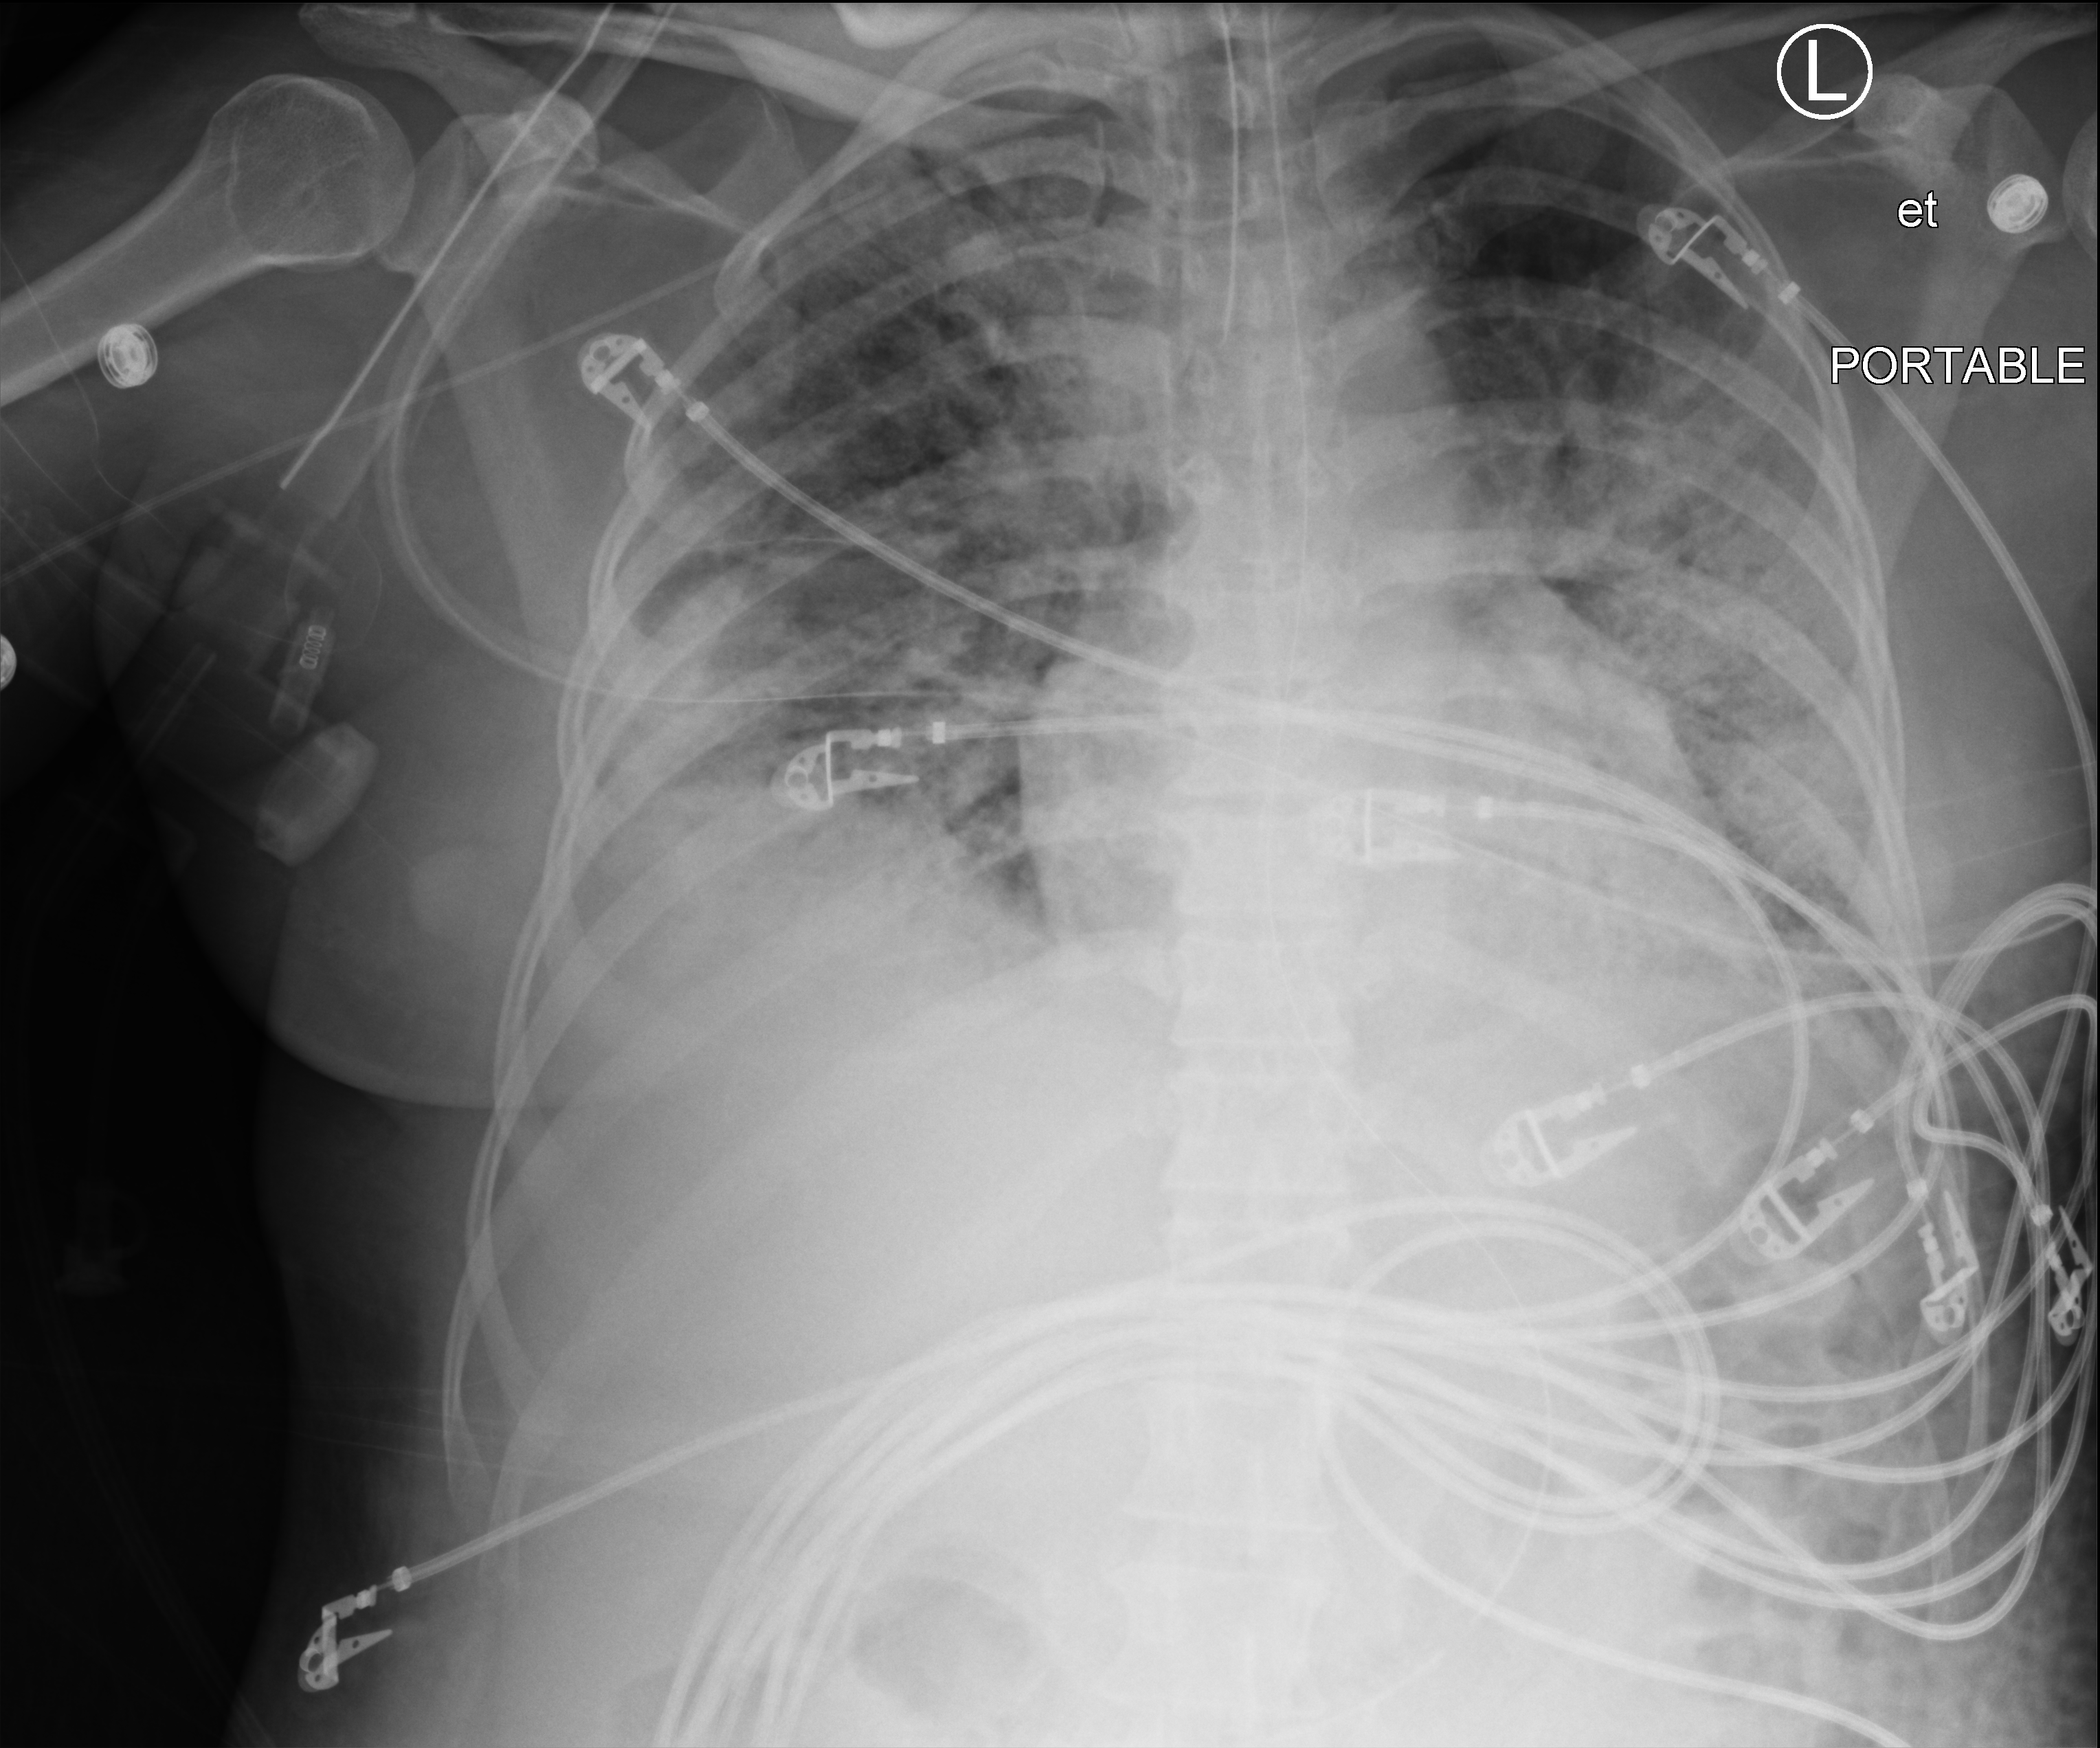
Bedside chest radiograph (computed radiography), anteroposterior (AP) projection. Female patient hospitalised with COVID-19, age 18–59 years.
Admission-level facts for this patient (not findings on this image; timing relative to this image not recorded): mechanically ventilated during this hospital stay: yes; diabetes (admission record): no.